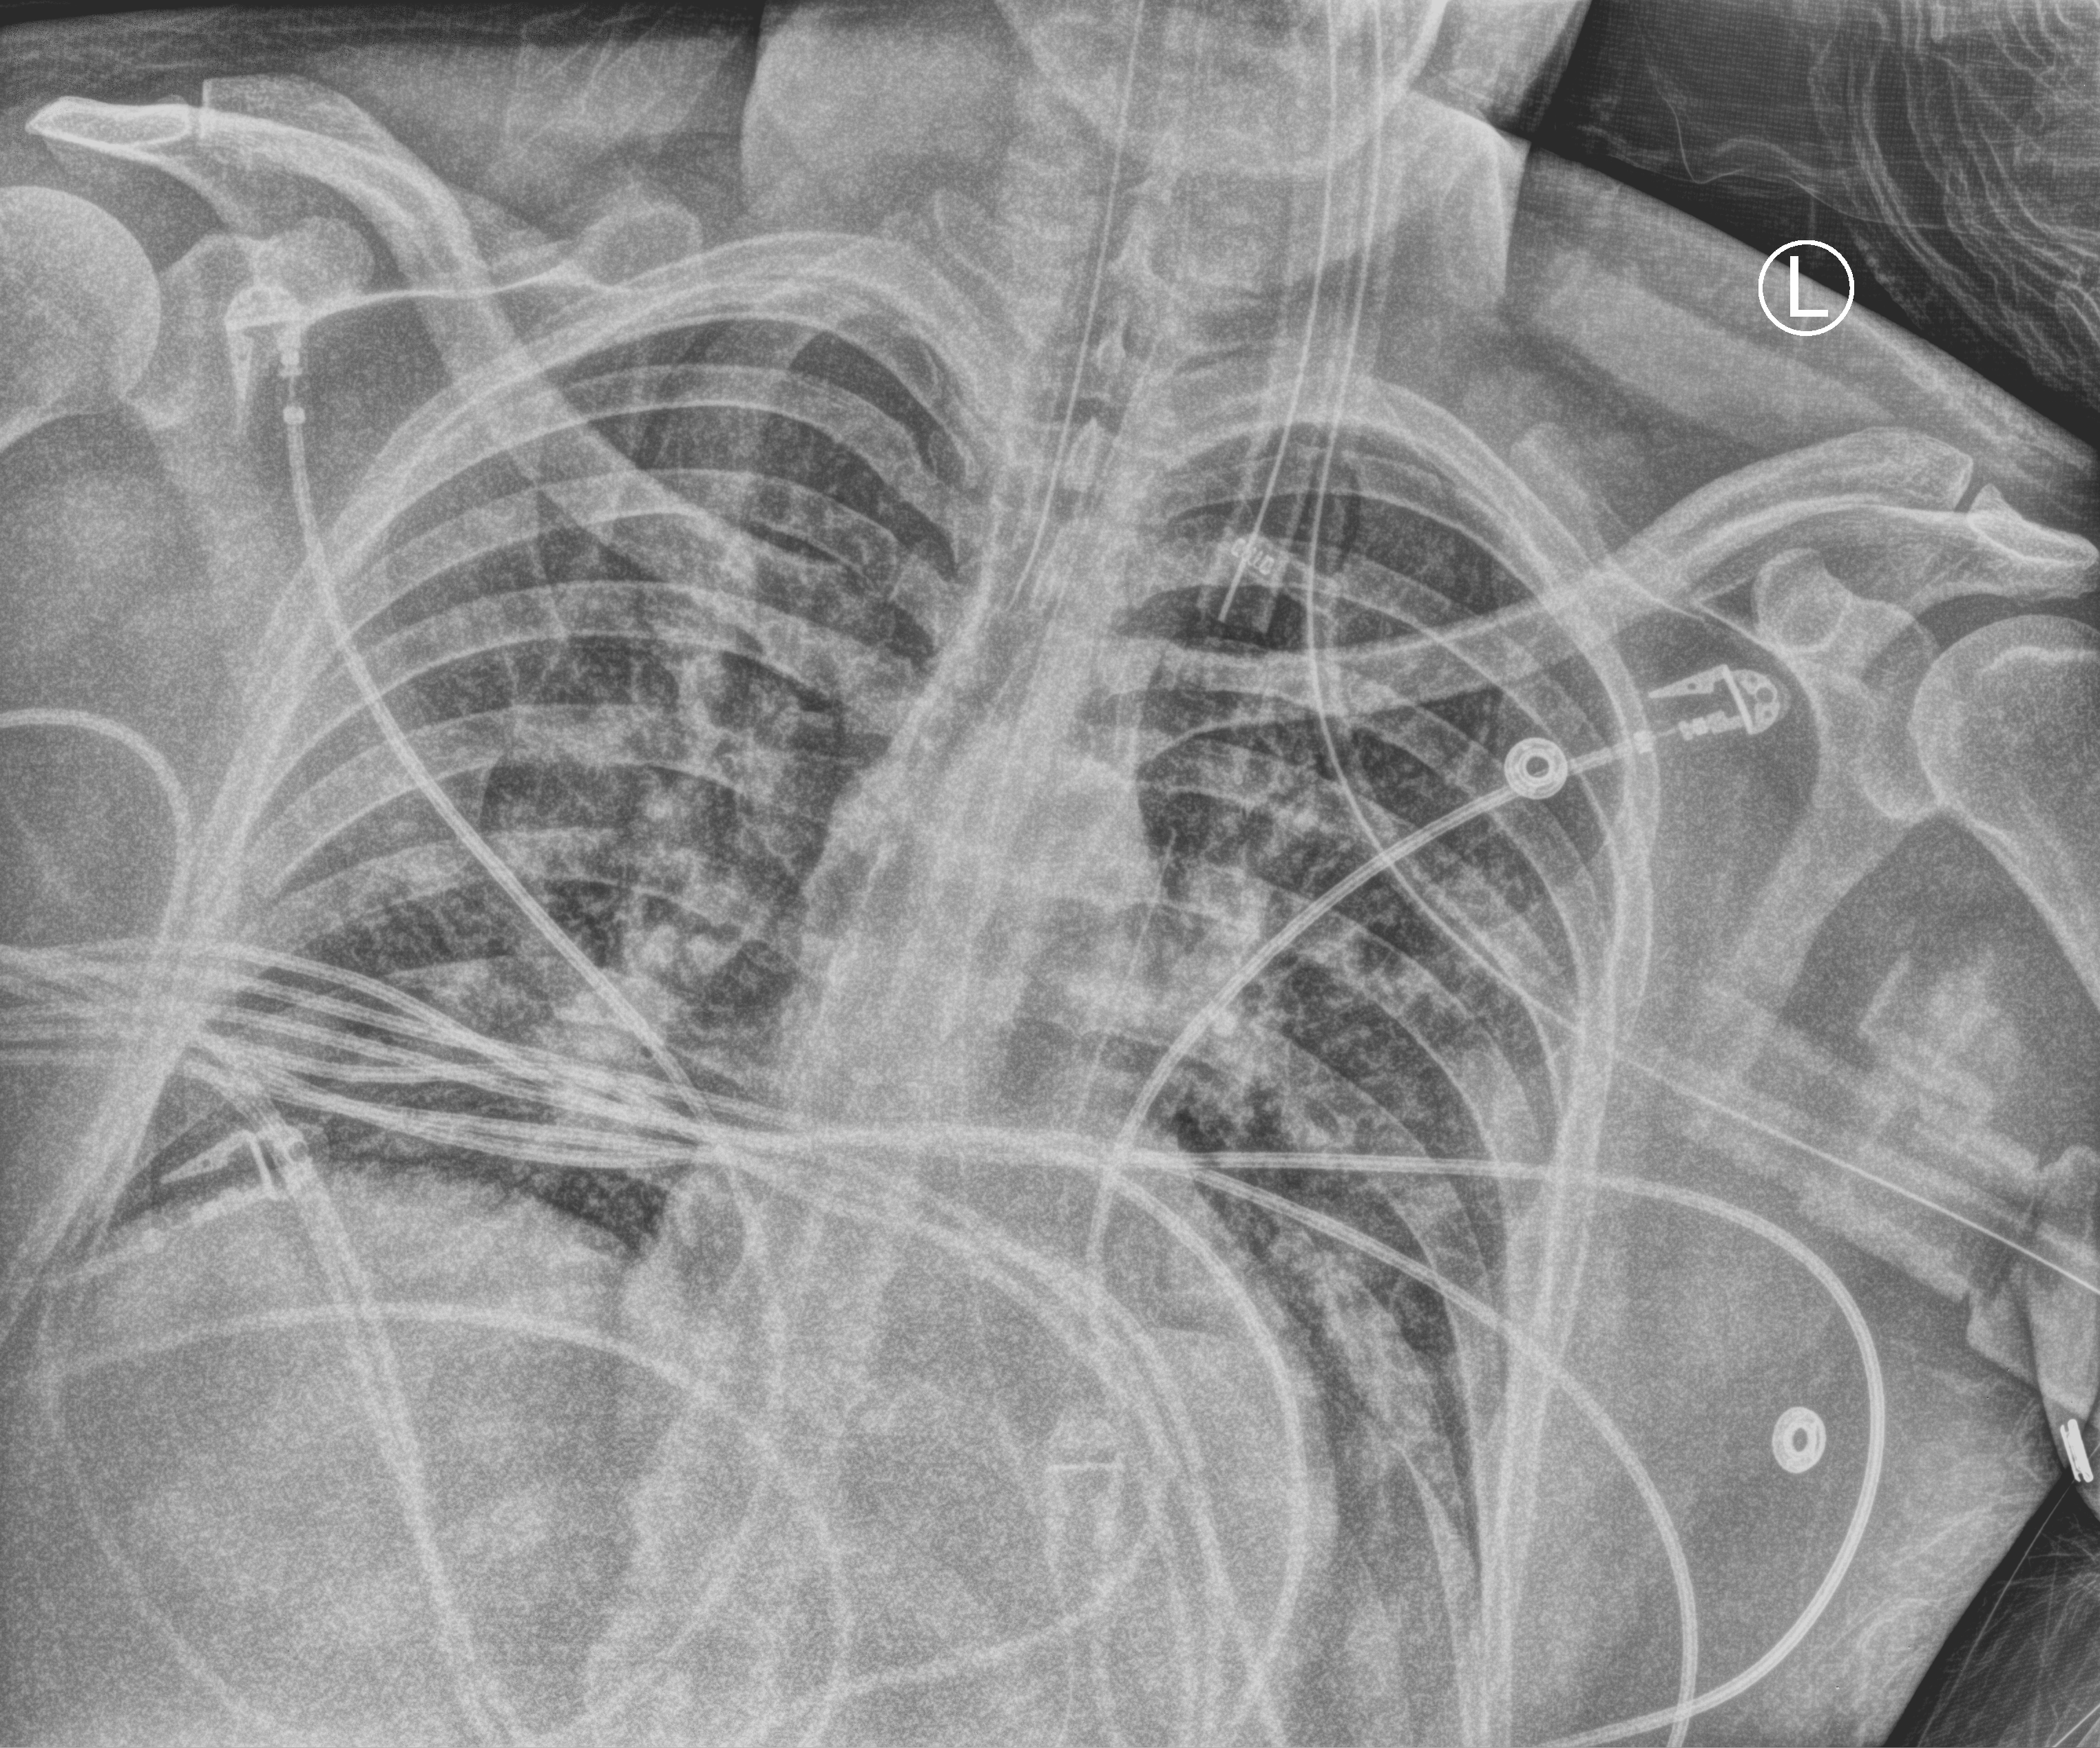
Bedside chest radiograph (computed radiography), anteroposterior (AP) projection. Male patient hospitalised with COVID-19, age 18–59 years.
From the hospital-stay record, not from the radiograph (when in the stay this image was taken is not recorded): hypertension (admission record): no.